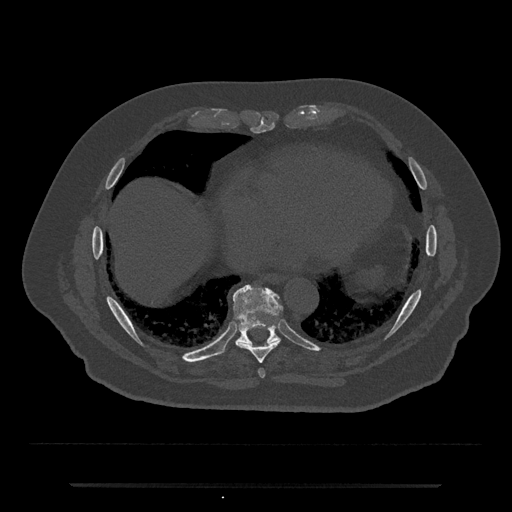
CT including the spine, one axial slice; position 786 of 797 along the scan axis; bone window (W 1800 / L 400 HU); 0.5 mm slice thickness; 512 × 512 image matrix. Male patient, age 80 years. From the clinical record (not read from this slice): primary cancer: prostate; vertebrae with lytic lesions (as recorded): L1, T11.
Outlined on this slice (semi-automatically segmented with operator editing):
- T8 vertebra: bounding box (x1, y1, x2, y2) in pixels: (236, 324, 279, 363)
- T9 vertebra: (222, 285, 283, 353)